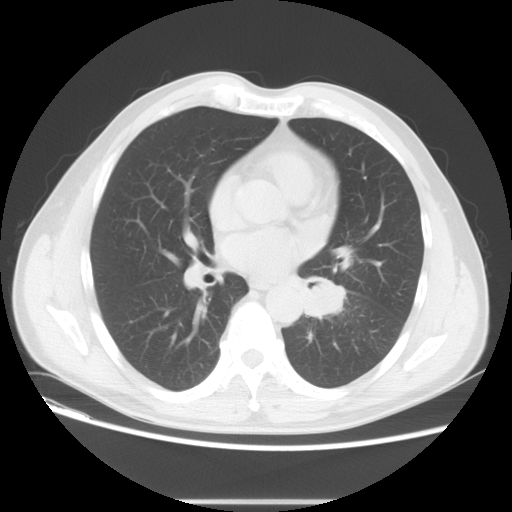
Chest CT, one axial slice; position 28 of 59 along the scan axis; reconstruction kernel STANDARD; 120 kVp; lung window (W 1500 / L -600 HU); 512 × 512 image matrix, field of view 378 × 378 mm. Male patient, age 59 years. Case-level facts recorded for this patient, not image findings: clinical TNM (as recorded): T2 N3 M0; histopathological grade: G3.
Annotated regions visible in this slice (rectangle marked by the reading radiologist):
- lung tumour (recorded histology: small cell carcinoma): box from (x=294, y=268) to (x=358, y=328) px